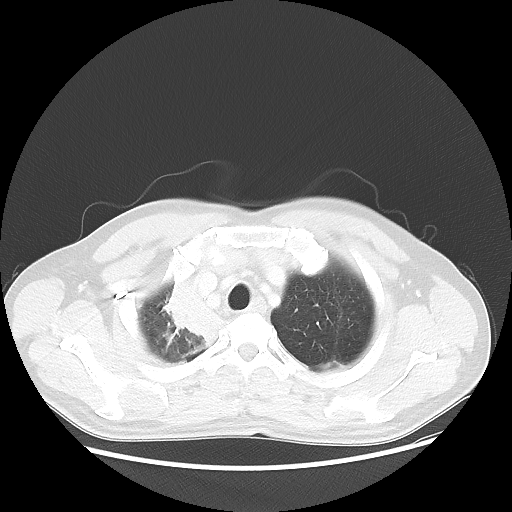
Chest CT, one axial slice; position 47 of 56 along the scan axis; reconstruction kernel LUNG; 100 kVp; lung window (W 1500 / L -600 HU); 5 mm slice thickness; 512 × 512 image matrix, field of view 398 × 398 mm. Patient: male, 60 years. From the clinical record (not read from this slice): clinical TNM (as recorded): T2a N1 M0.
Outlined on this slice (rectangle marked by the reading radiologist):
- lung tumour (recorded histology: squamous cell carcinoma): box from (x=154, y=271) to (x=235, y=365) px